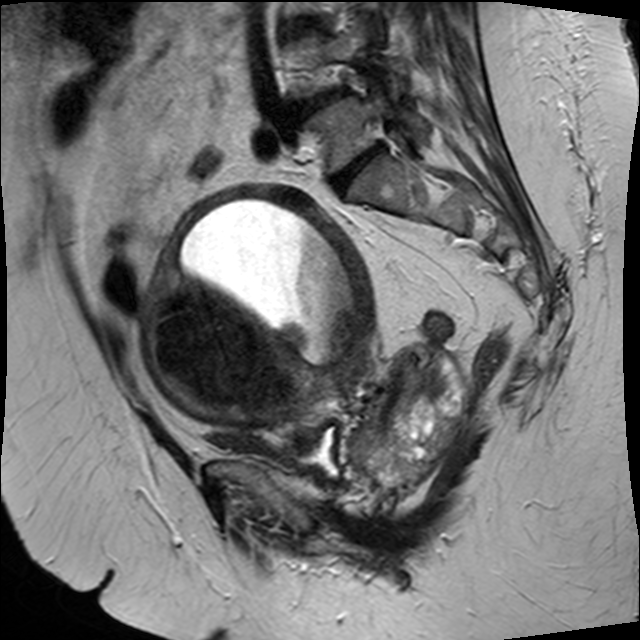
Pelvic MRI for cervical cancer, one sagittal slice. Position 21 of 34 along the scan axis. T2-weighted. 1.5 T. TE 89 ms, TR 3320 ms. 4 mm slice thickness. 640 × 640 image matrix, field of view 260 × 260 mm. Female patient, age 50 years.
Structures marked on this image (expert manual segmentation):
- uterus and cervix: box from (x=144, y=185) to (x=469, y=484) px